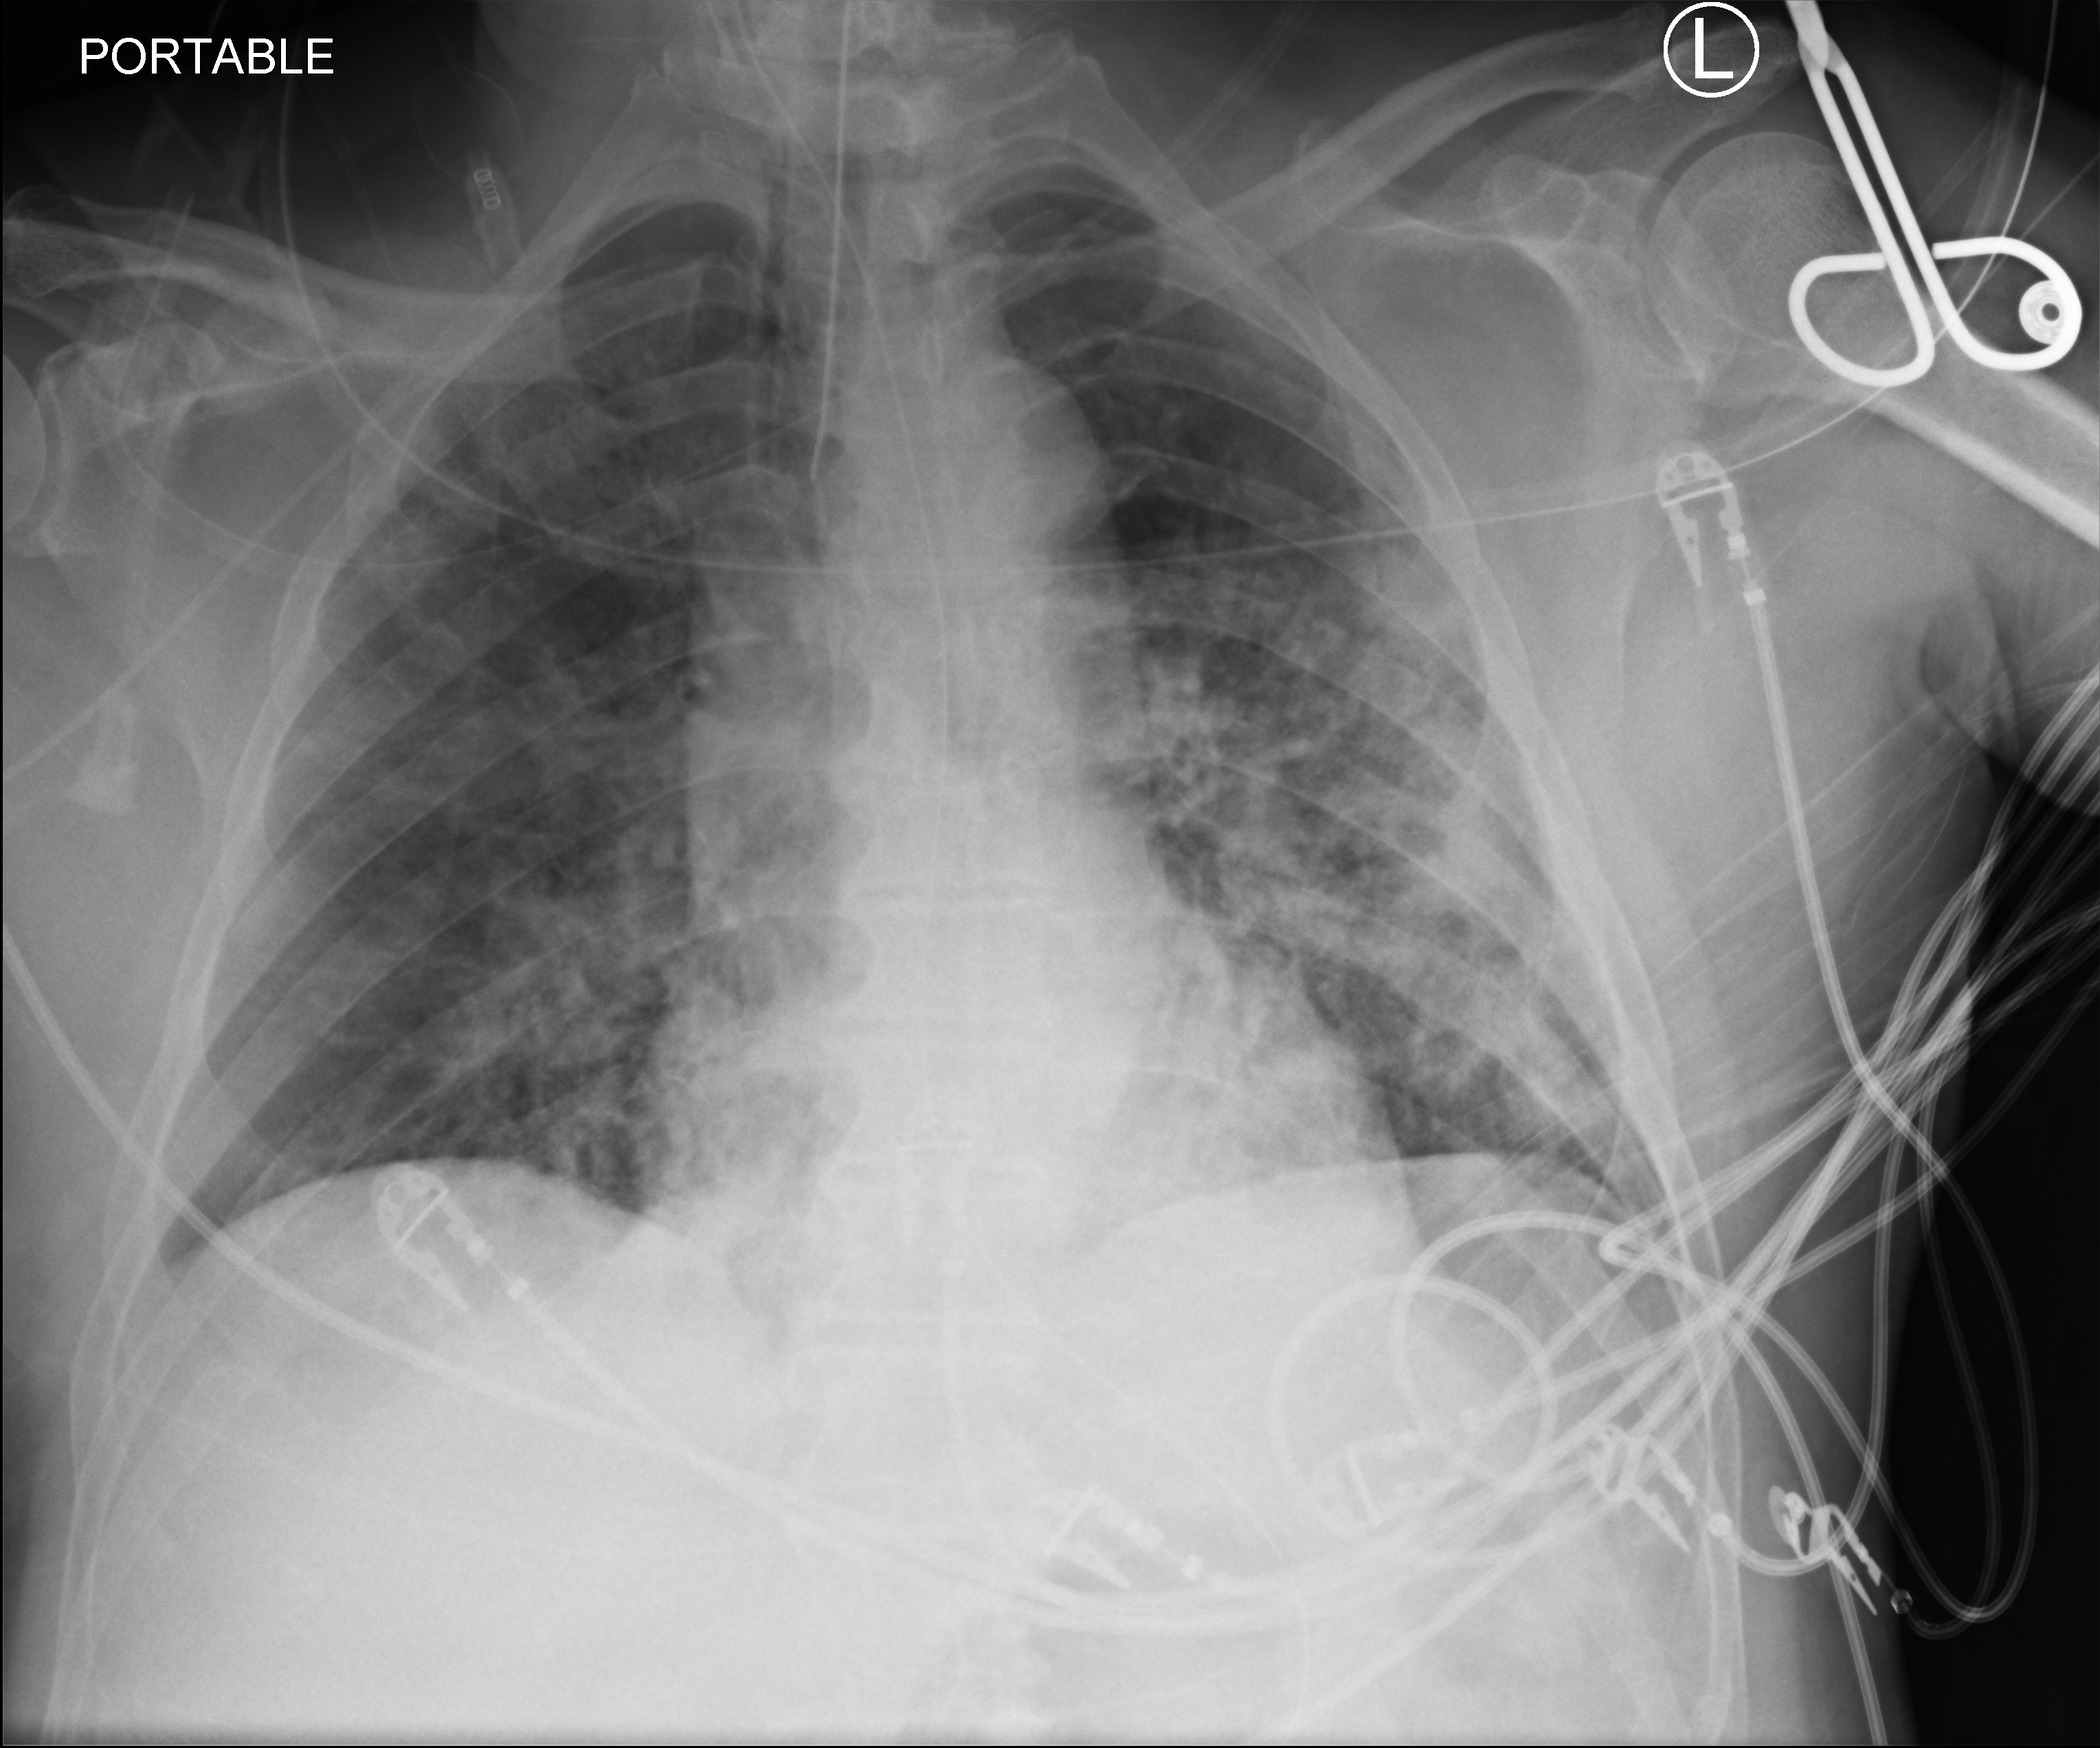
Chest X-ray (portable), anteroposterior (AP) projection. Patient hospitalised with COVID-19; male, aged 60–74 years.
From the hospital-stay record, not from the radiograph (when in the stay this image was taken is not recorded):
- COPD (admission record): no
- length of hospital stay: 20 days